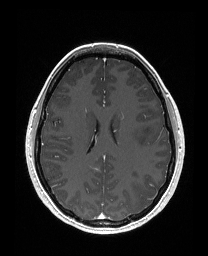
Brain MRI from a brain-tumour surgery series, one axial slice. T1-weighted post-contrast. 1 mm slice thickness. 208 × 256 image matrix, field of view 203 × 250 mm. Case-level facts recorded for this patient, not image findings: histopathology: Astrocytoma; WHO grade: 3; IDH mutation: yes; tumour location: Left Frontal.
Structures marked on this image (expert manual segmentation):
- tumour: bounding box (x1, y1, x2, y2) in pixels: (130, 124, 157, 146)